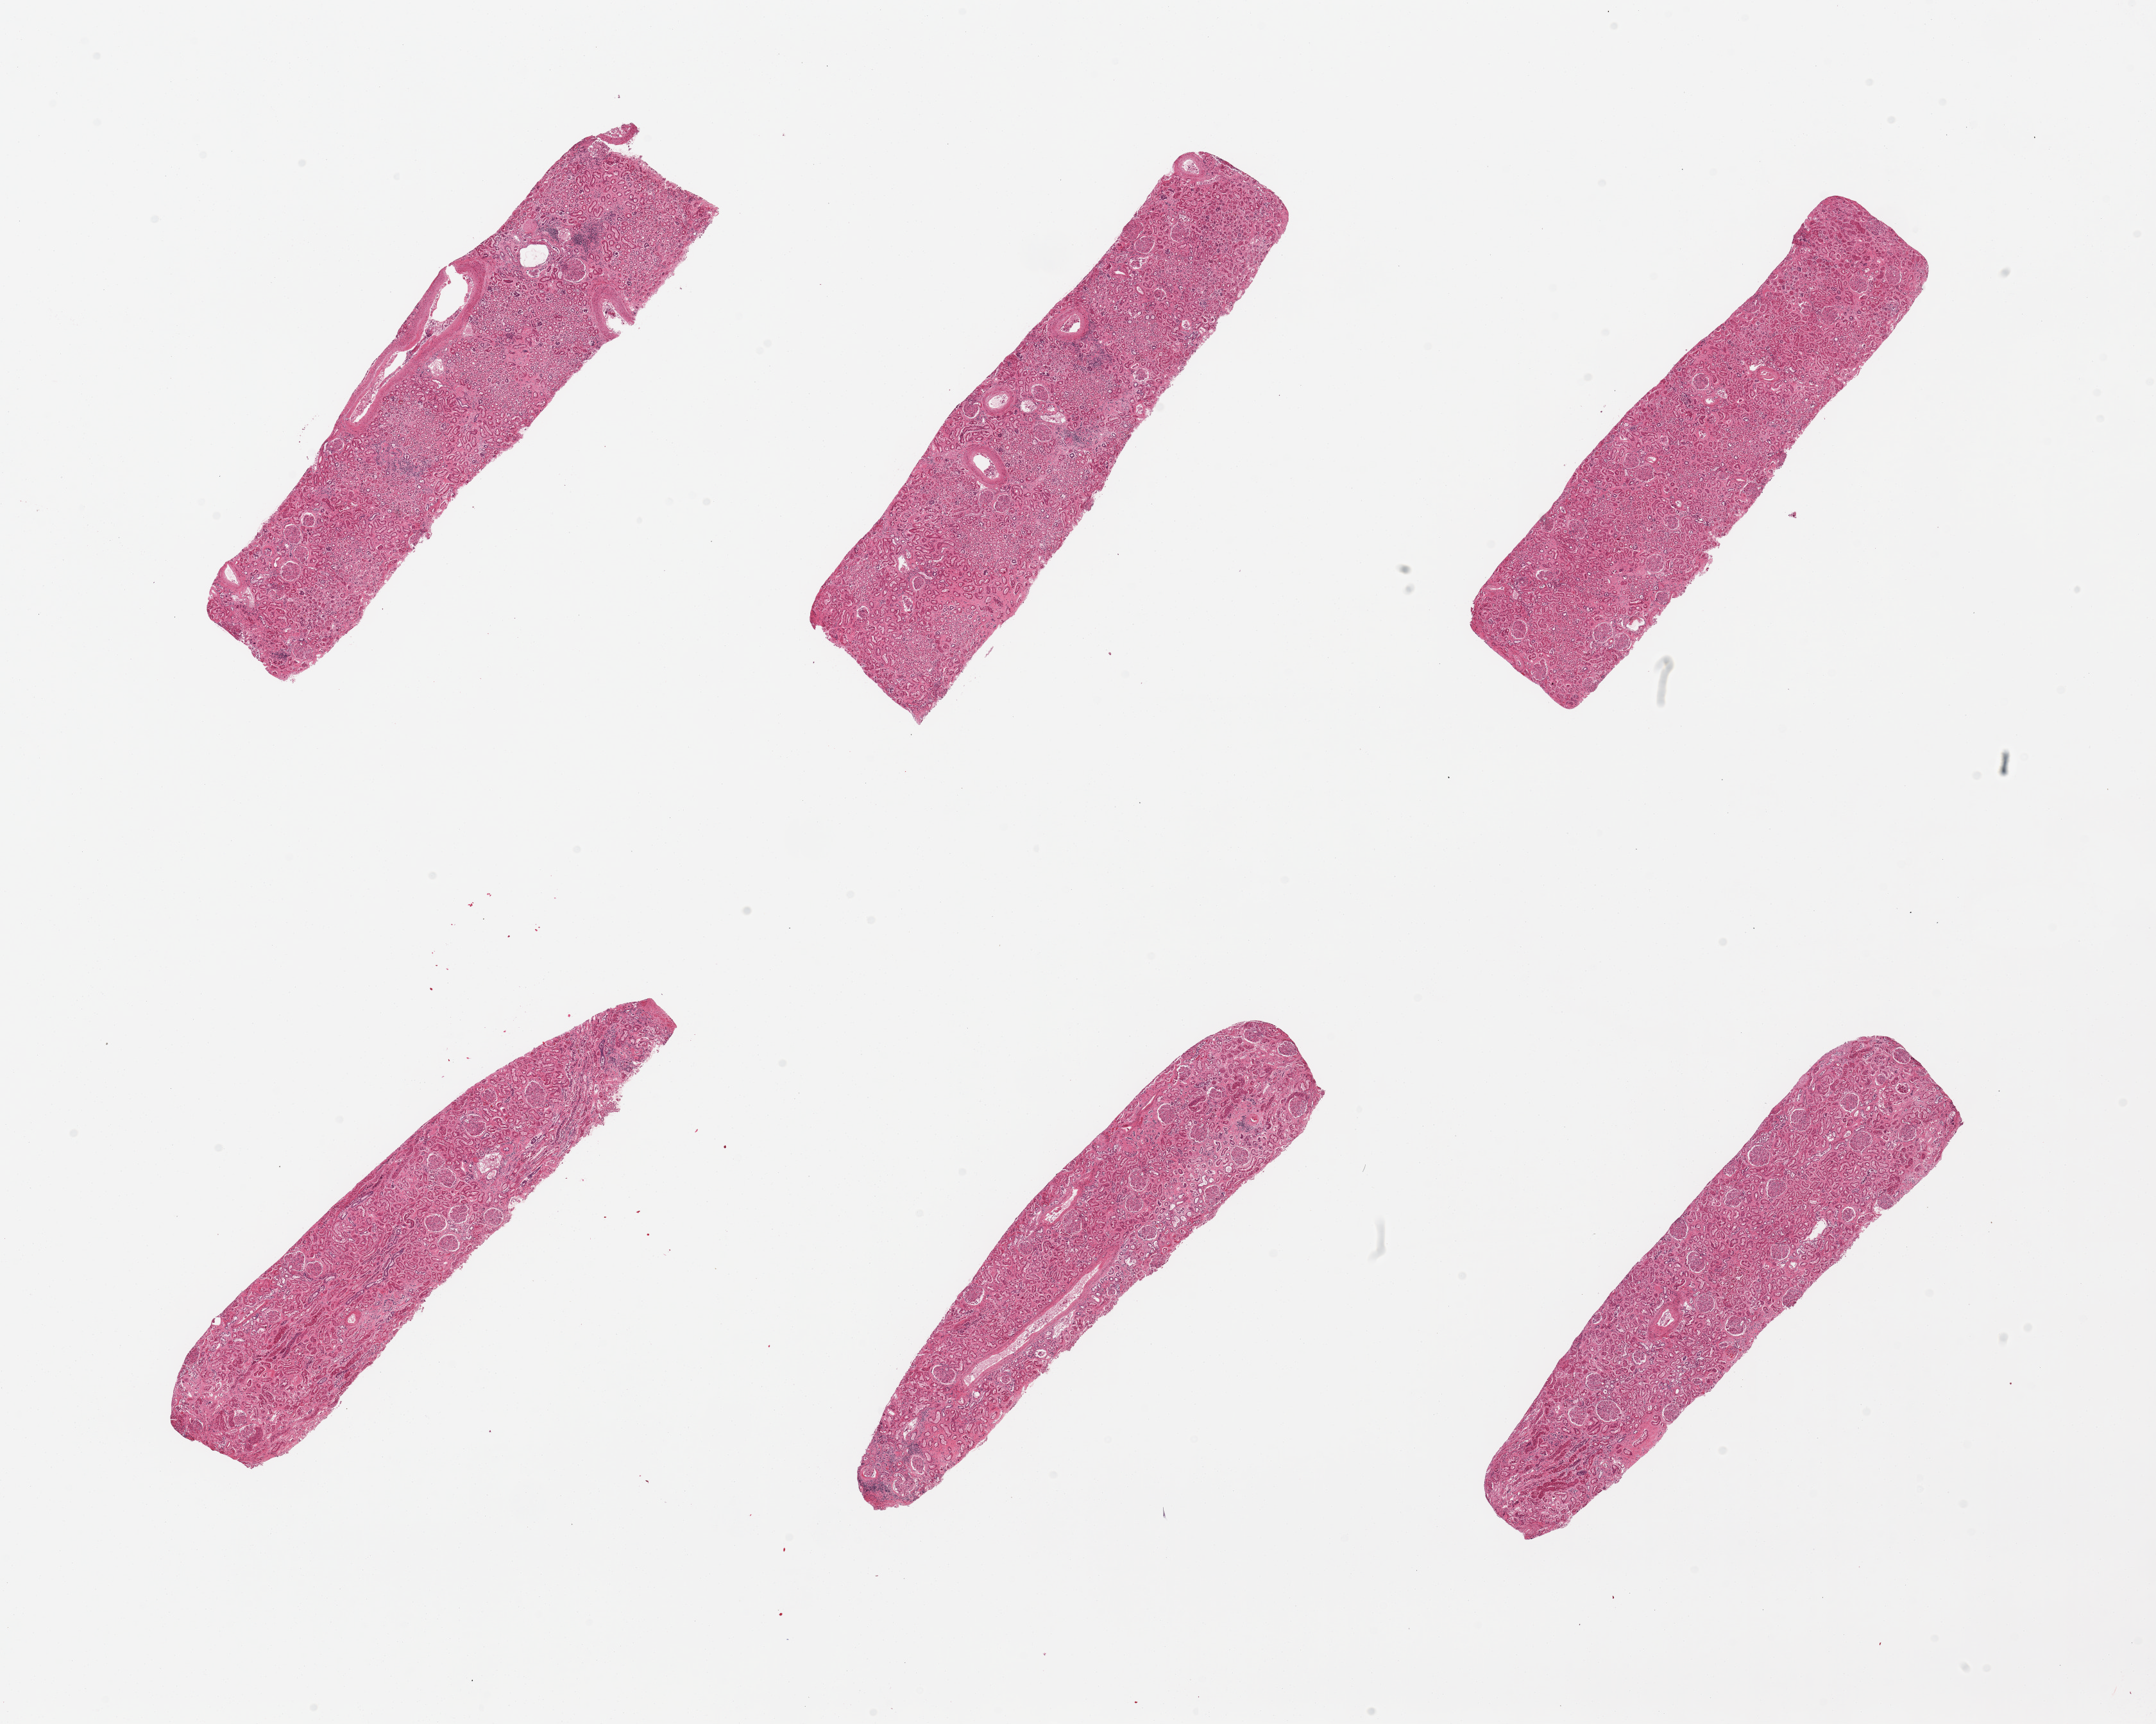
Whole-slide image, H&E stain, shown as a low-resolution overview of the whole scanned area (about 26.6 x 21.2 mm). PAXgene-fixed paraffin-embedded (PFPE) section. Target tissue: renal cortex. Tissue donor sample. Donor: male.
* pathologist's review note for this sample: 6 pieces, glomeruli present, tubules moderate-marked autolyzed